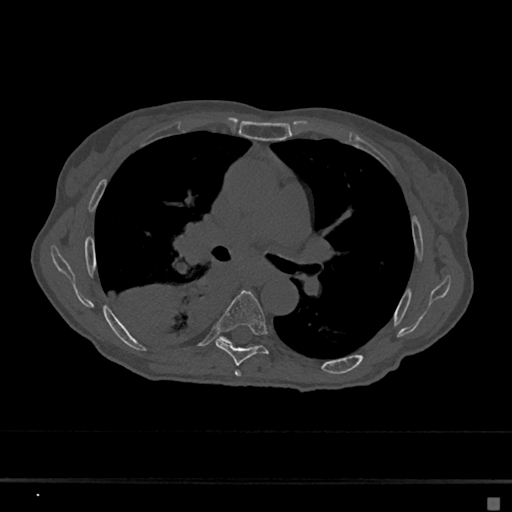
CT including the spine, one axial slice; slice 412 of 797 in the series (ordered by position); reconstruction kernel Br40s/3; bone window (W 1800 / L 400 HU); 0.5 mm slice thickness; 512 × 512 image matrix, field of view 360 × 360 mm. Female patient, age 68 years. From the clinical record (not read from this slice): primary cancer: renal.
Structures marked on this image (semi-automatic segmentation, software-assisted and operator-edited):
- T5 vertebra: bounding box [x1, y1, x2, y2] px = [235, 370, 241, 377]
- T6 vertebra: [215, 291, 269, 366]
- T7 vertebra: [221, 337, 231, 343]